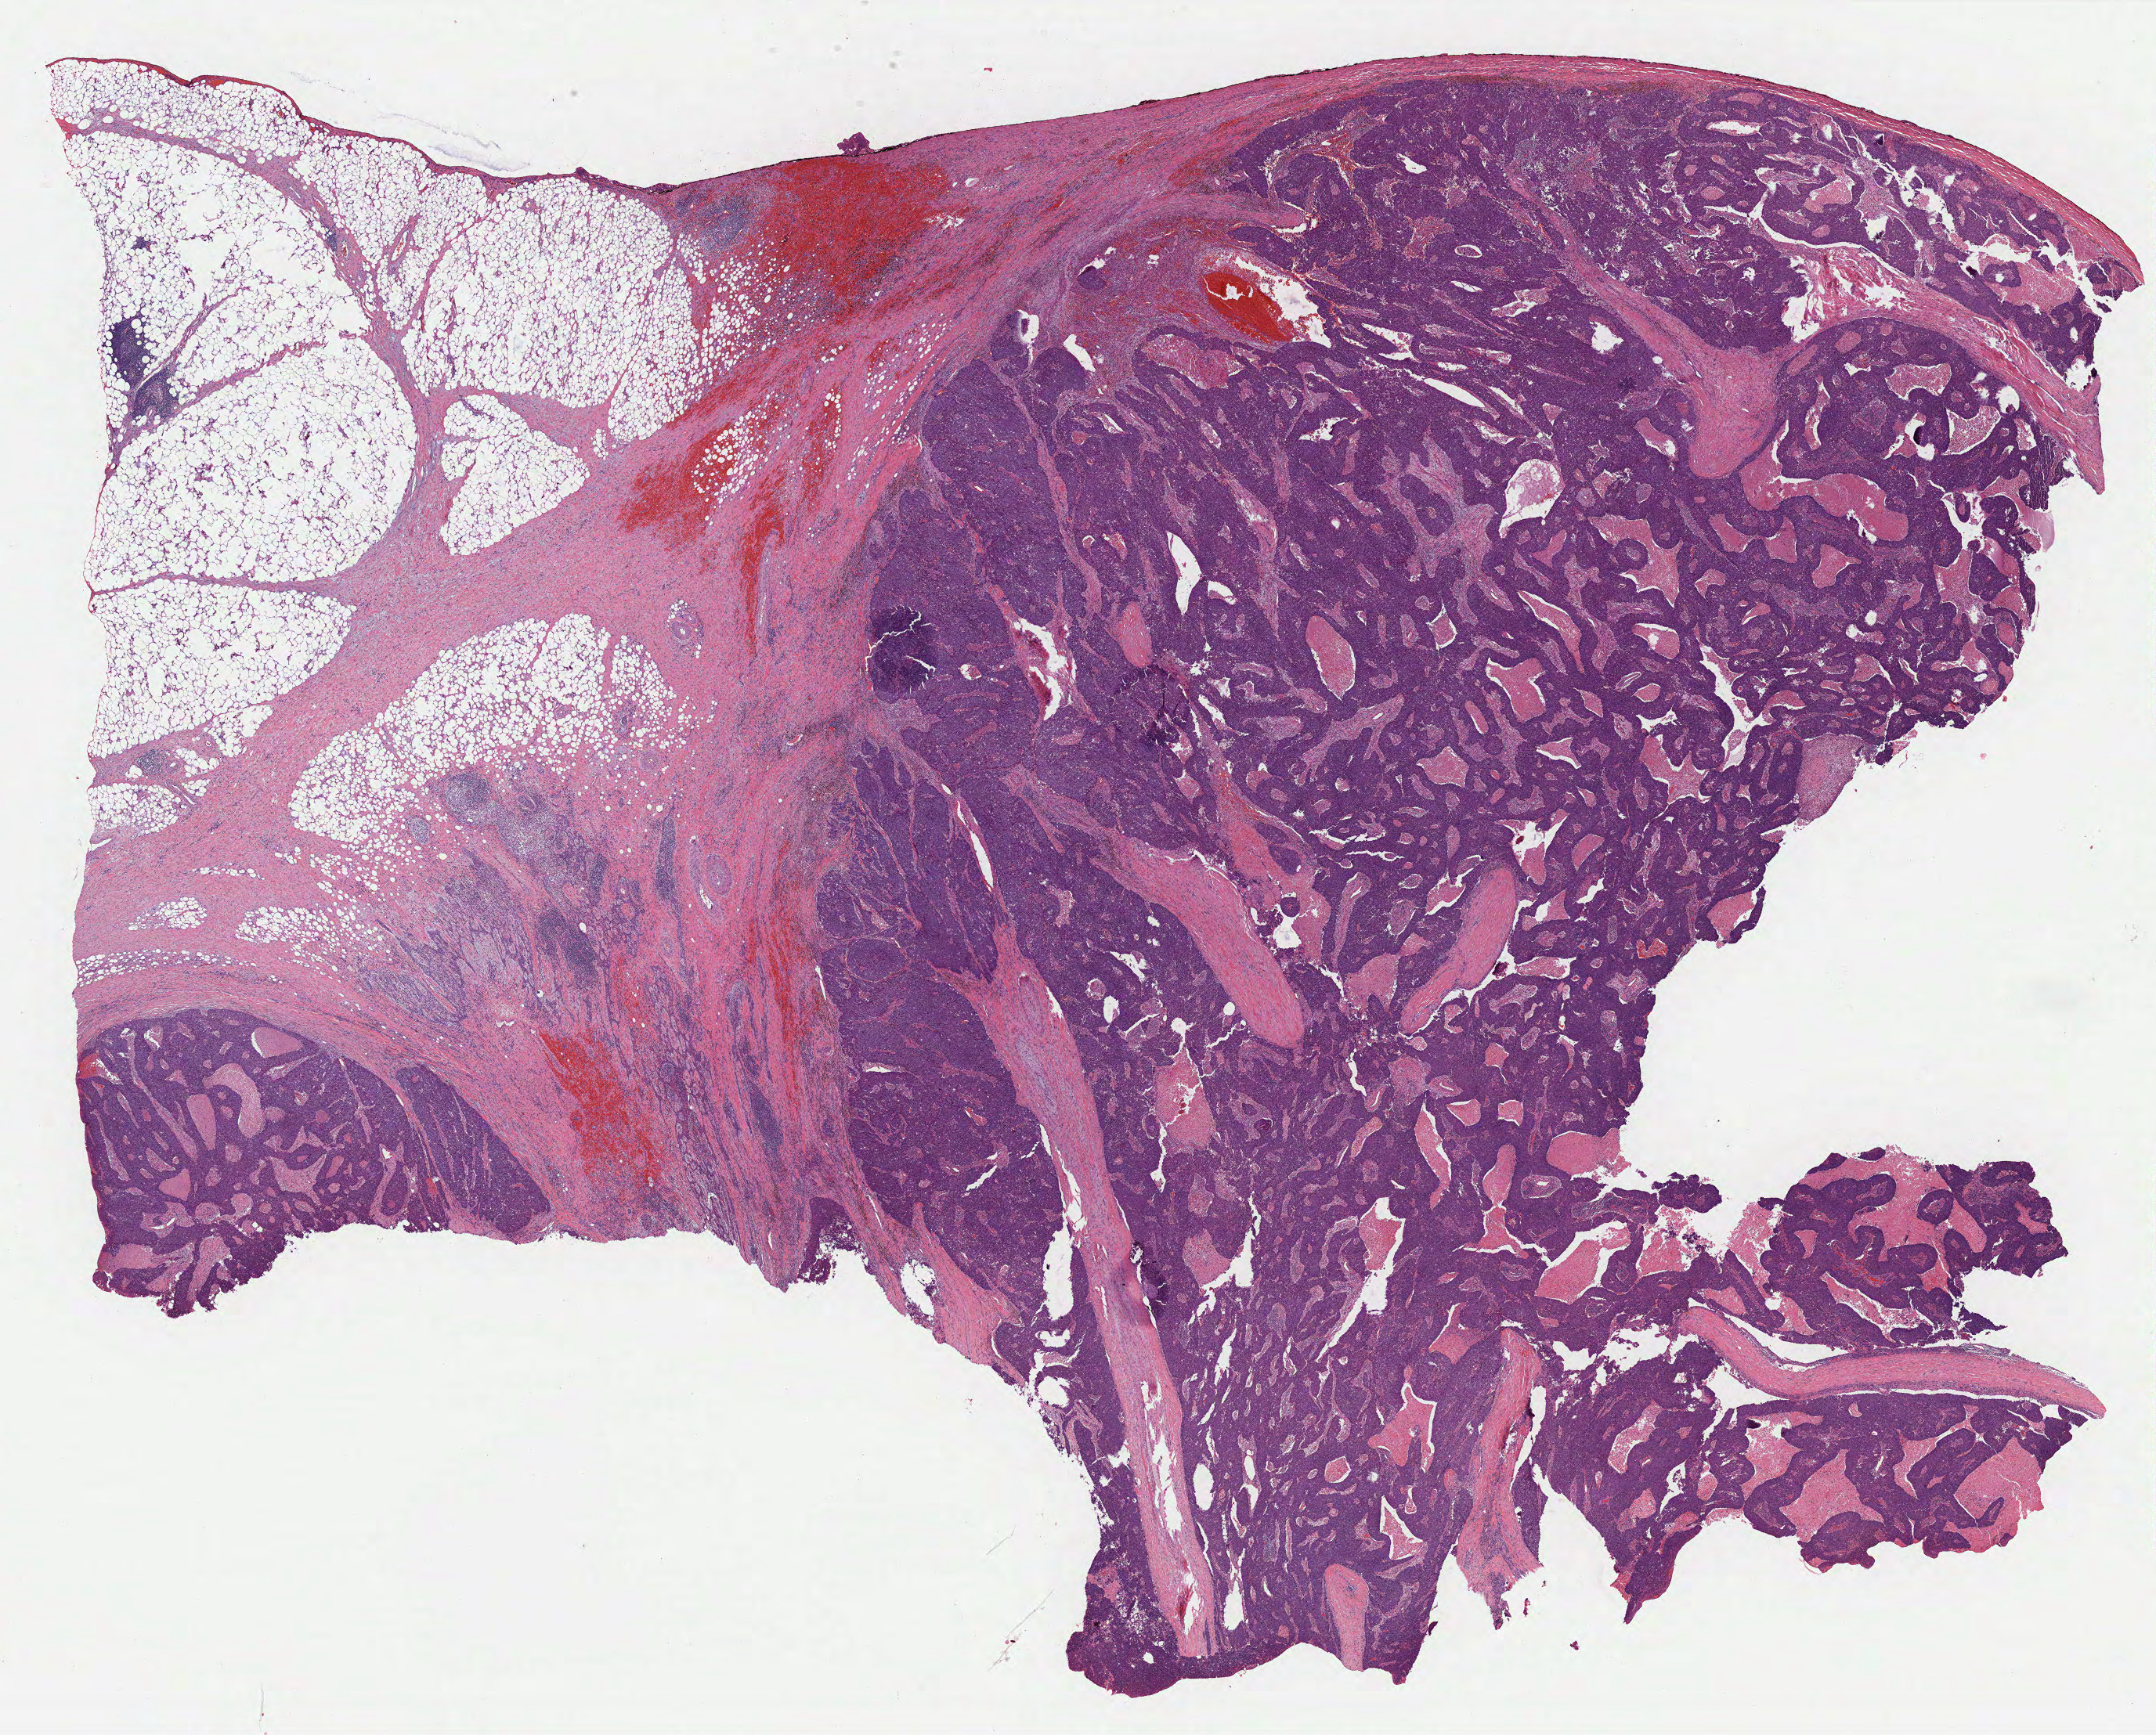
Digitized H&E tissue section (whole slide) — shown as a low-resolution overview of the whole scanned area (about 22.4 x 18.1 mm); FFPE section; thymus, primary tumour sample. Male, age 63 years at initial diagnosis.
Pathologic diagnosis: Thymic carcinoma, NOS.